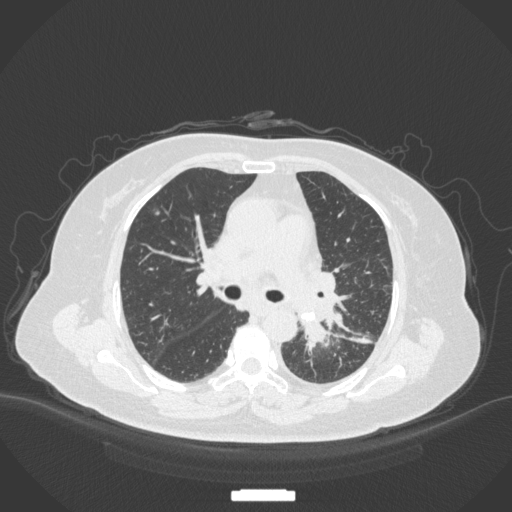
Chest CT, one axial slice. Reconstruction kernel B31f. 120 kVp. Lung window (W 1500 / L -600 HU). 1 mm slice thickness. 512 × 512 image matrix, field of view 400 × 400 mm. Female patient, age 69 years. Case-level facts recorded for this patient, not image findings: clinical TNM (as recorded): T2b N3 M1.
Outlined on this slice (bounding box drawn by a radiologist):
- lung tumour (recorded histology: adenocarcinoma): bounding box [x1, y1, x2, y2] px = [298, 314, 335, 352]